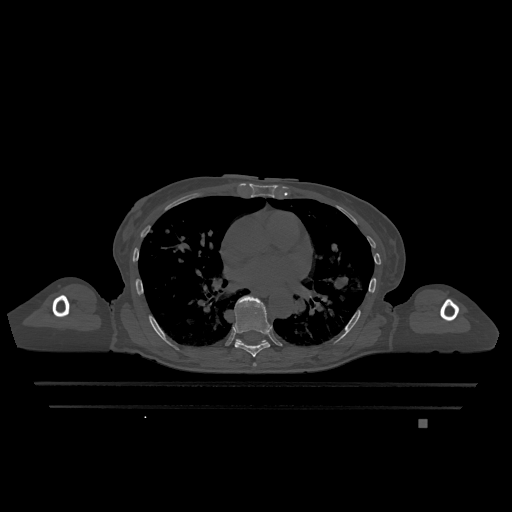
CT including the spine, one axial slice. Slice 730 of 1317 in the series (ordered by position). Bone window (W 1800 / L 400 HU). 0.5 mm slice thickness. 512 × 512 image matrix, field of view 500 × 500 mm. Patient: female, 74 years. Case-level facts recorded for this patient, not image findings: primary cancer: lung; vertebrae with lytic lesions (as recorded): T1, T4, T5, T6, L4, L5.
Outlined on this slice (semi-automatic segmentation, software-assisted and operator-edited):
- T6 vertebra: box from (x=253, y=363) to (x=256, y=367) px
- T7 vertebra: (x=234, y=296)–(x=270, y=357)
- T9 vertebra: (x=236, y=339)–(x=267, y=343)